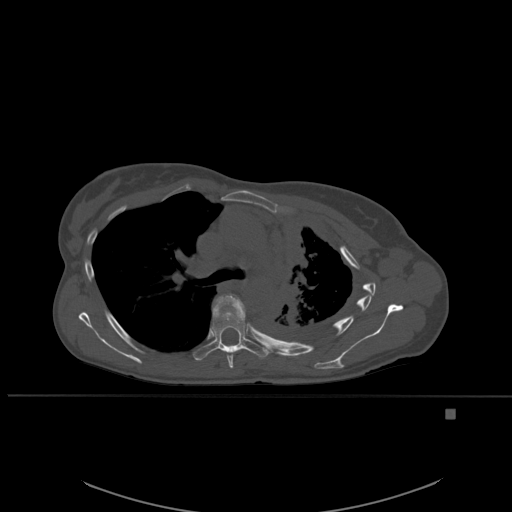
CT including the spine, one axial slice. Position 388 of 537 along the scan axis. Bone window (W 1800 / L 400 HU). 512 × 512 image matrix, field of view 440 × 440 mm. Patient: female, 45 years. From the clinical record (not read from this slice): primary cancer: lung.
Structures marked on this image (semi-automatically segmented with operator editing):
- T5 vertebra: bounding box (x1, y1, x2, y2) in pixels: (213, 294, 245, 369)
- T6 vertebra: (196, 305, 269, 361)